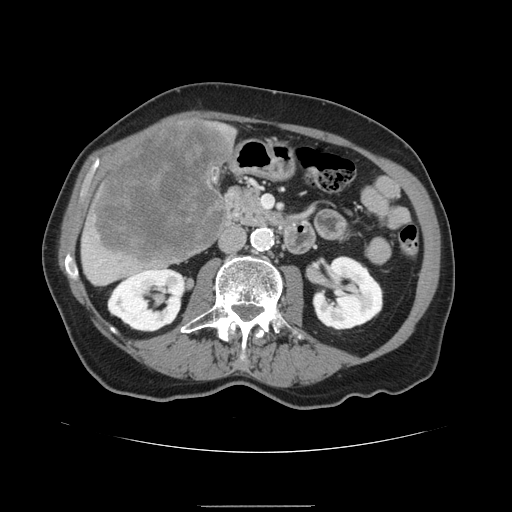
Contrast-enhanced abdominal CT, one axial slice; position 51 of 168 along the scan axis; soft-tissue window (W 400 / L 40 HU); 512 × 512 image matrix. Male patient, age 74 years. Case-level facts recorded for this patient, not image findings: diagnosis: colorectal cancer liver metastases, imaged before liver resection; multiple liver metastases: no; largest metastasis: 14.5 cm; disease in both lobes: yes.
Annotated regions visible in this slice (manually delineated by an expert):
- liver: box from (x=81, y=117) to (x=237, y=286) px
- liver metastasis: (x=93, y=121)–(x=232, y=265)